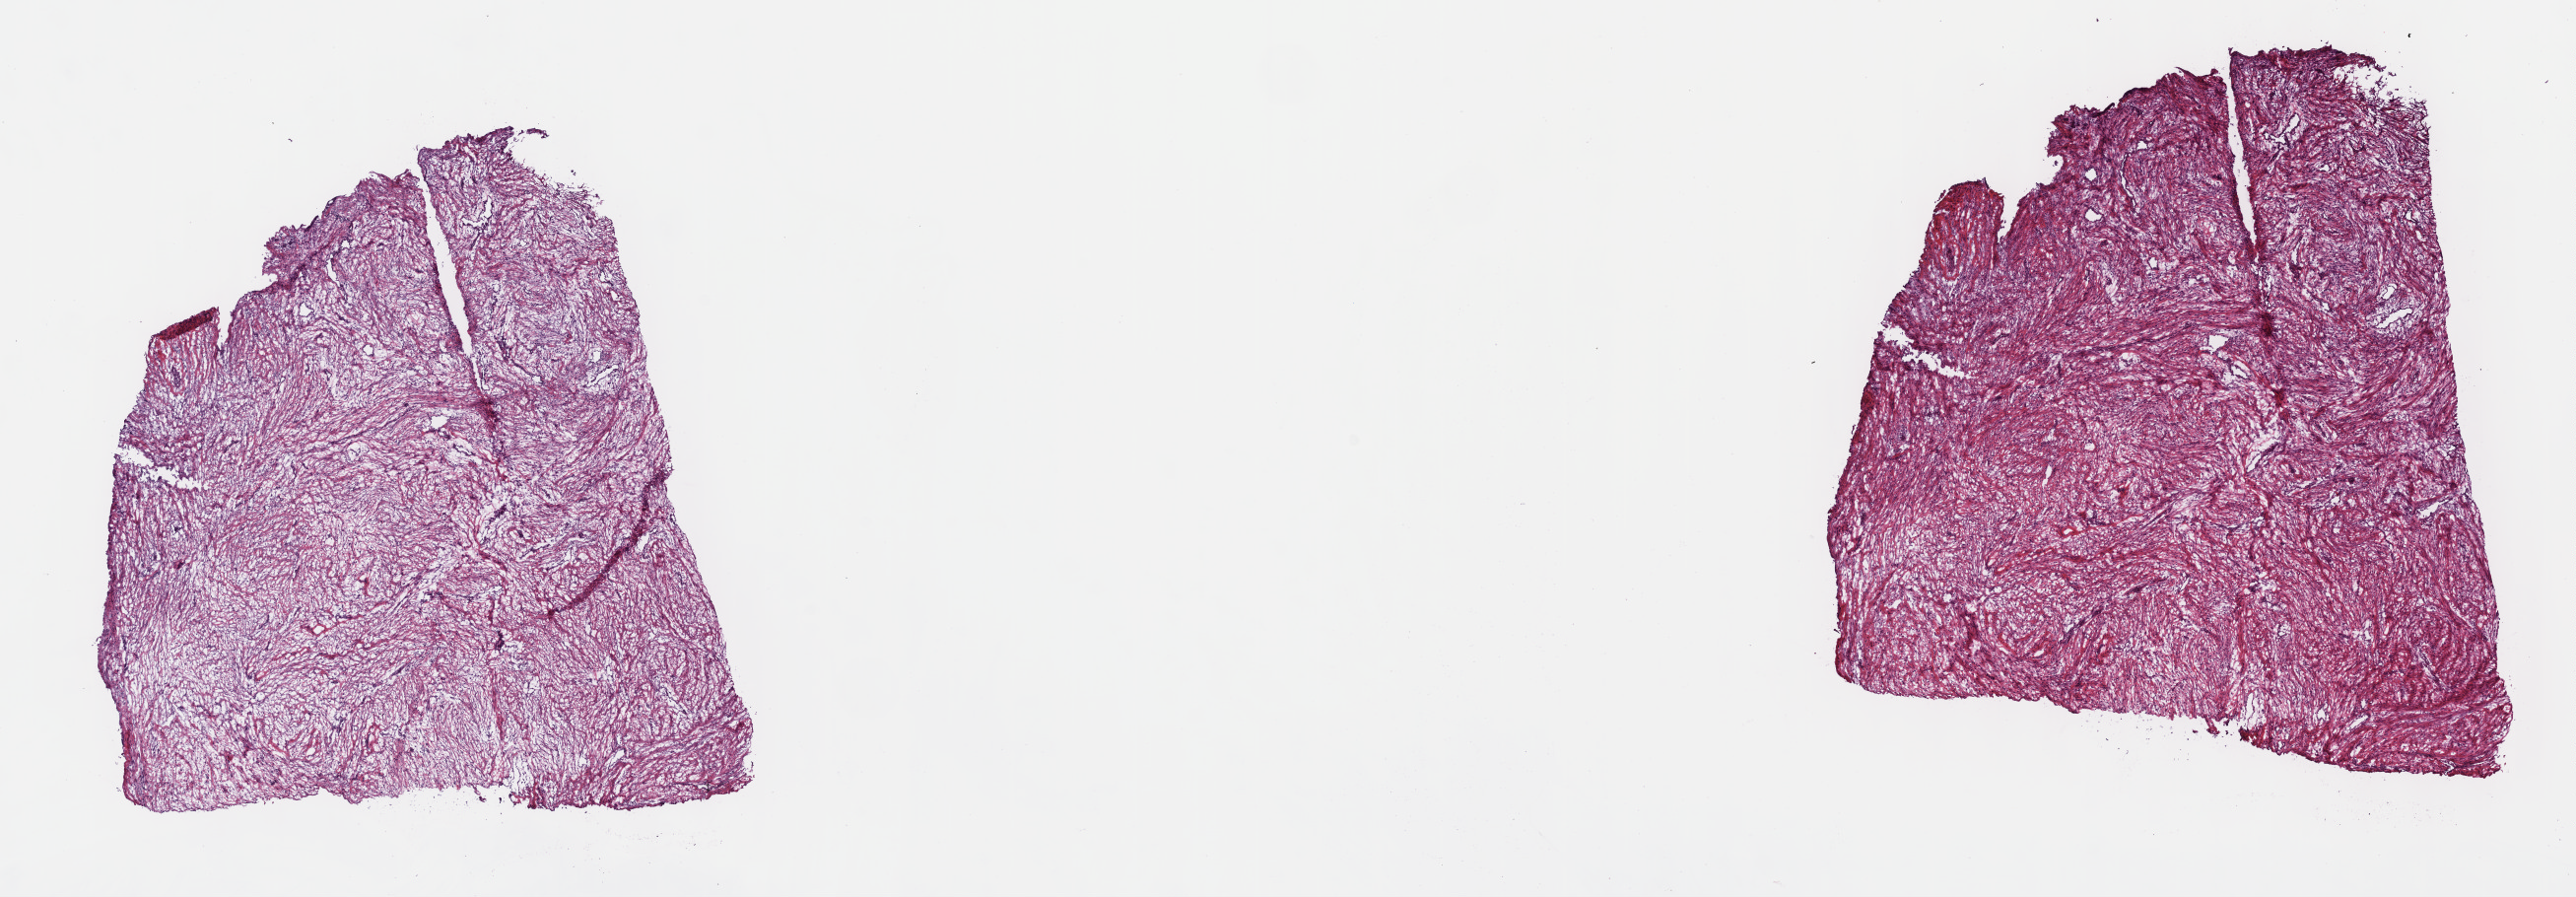
Whole-slide histology image, H&E, shown as a low-resolution overview of the whole scanned area (about 21.1 x 7.4 mm, from a 40x scan), frozen section from the top of the tissue portion, retroperitoneum and peritoneum, primary tumour sample. Male, age 56 years at initial diagnosis. Pathologist review of this section (percent, as recorded): tumour cells 80%, tumour nuclei 80%, normal cells 0%, stromal cells 20%, necrosis 0%. Inflammatory infiltration, as recorded: lymphocyte infiltration 3%, monocyte infiltration 1%, neutrophil infiltration 2%.
Pathologic diagnosis: Abdominal fibromatosis.